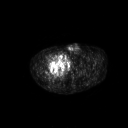
FDG PET of an extremity soft-tissue mass (from a PET/CT study), one axial slice; slice 283 of 311 in the series (ordered by position); 3.27 mm slice thickness; 128 × 128 image matrix. Patient: male, 50 years. Case-level facts recorded for this patient, not image findings: histological type: undifferentiated - pleiomorphic; grade: high; site of the primary tumour: right thigh.
Outlined on this slice (expert contour drawn on MRI and transferred to this co-registered scan by the dataset authors):
- gross tumour volume including surrounding oedema: bounding box (x1, y1, x2, y2) in pixels: (51, 53, 65, 68)
- gross tumour volume (mass): (51, 54, 65, 67)